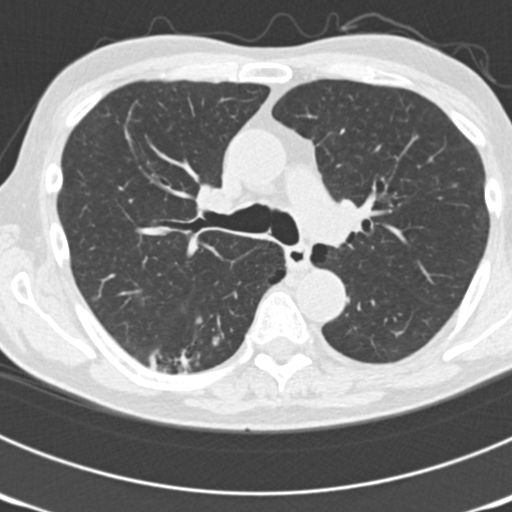
Chest CT (low-dose screening protocol), one axial image; third annual screen; lung window (W 1500 / L -600 HU); 2 mm slice thickness. Male, age 70 years at enrolment. Current smoker at enrolment.
• Expert reader's lesion annotation, bounding box [x1, y1, x2, y2] px = [140, 314, 236, 387].
• The screening reader recorded 3 non-calcified nodules or masses ≥4 mm on this exam (right upper lobe, left upper lobe, right lower lobe); which of them this box marks is not recorded.
• Participant outcome: lung cancer diagnosed 14 days after this screen — bronchiolo-alveolar adenocarcinoma, NOS, right lower lobe, poorly differentiated (G3), stage IB (AJCC 6th edition), 30 mm at pathology.